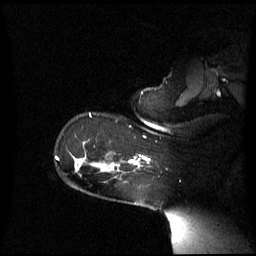
Breast MRI (dynamic contrast-enhanced), one sagittal slice; position 49 of 60 along the scan axis; dynamic contrast-enhanced series, image 2 of 3 at this slice position (ordered by acquisition); 1.5 T; TE 4.2 ms, TR 8.4 ms; 2.6 mm slice thickness; 256 × 256 image matrix, field of view 270 × 270 mm. Patient: female, 39 years. From the clinical record (not read from this slice): setting: breast cancer imaged before/during neoadjuvant chemotherapy; receptor status: triple-negative.
Structures marked on this image (semi-automatically segmented with operator editing):
- analysis volume of interest (the breast-tissue region the enhancement analysis was run in; not a lesion): bounding box (x1, y1, x2, y2) in pixels: (117, 156, 150, 173)
- tumour enhancement mask (voxels above the 70 % enhancement threshold inside the analysis volume of interest): (129, 156, 149, 164)